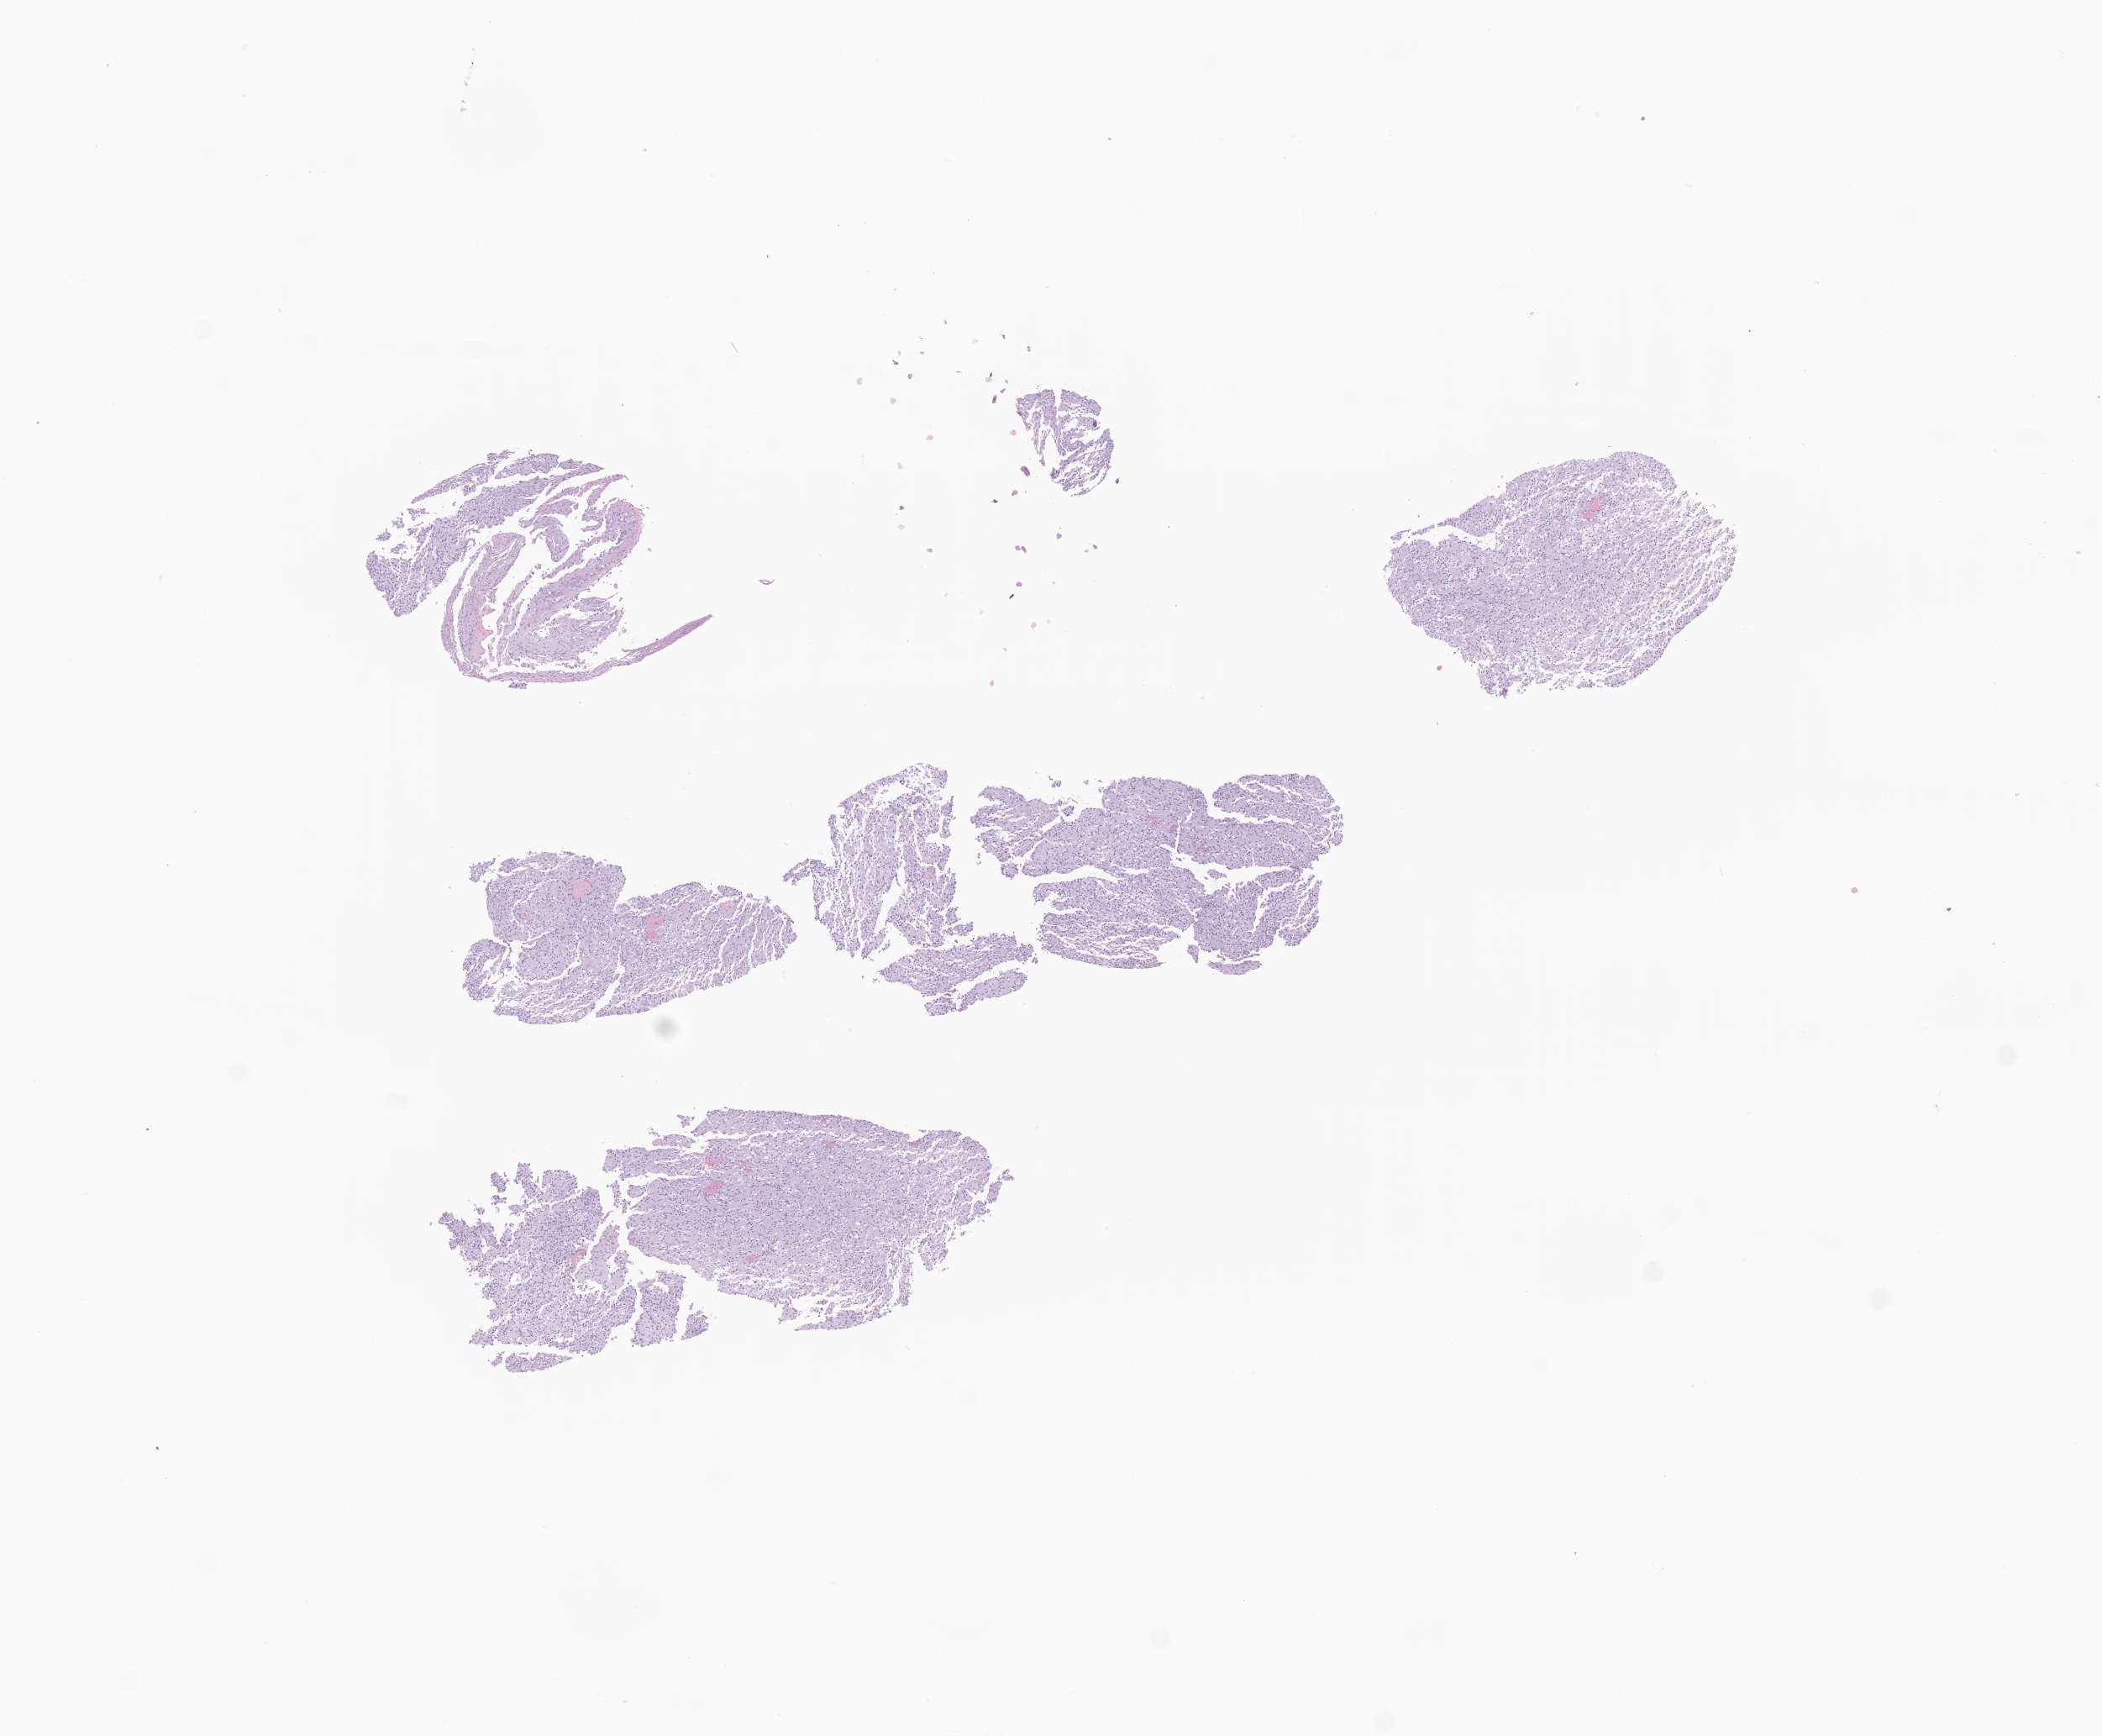
Haematoxylin and eosin whole-slide image of tumor tissue from the brain, shown as a low-resolution overview of the whole scanned area (about 10.5 x 8.7 mm); formalin-fixed paraffin-embedded section. Male patient, age 78 months (6 years 6 months).
Recorded diagnosis: Dysembryoplastic neuroepithelial tumor.